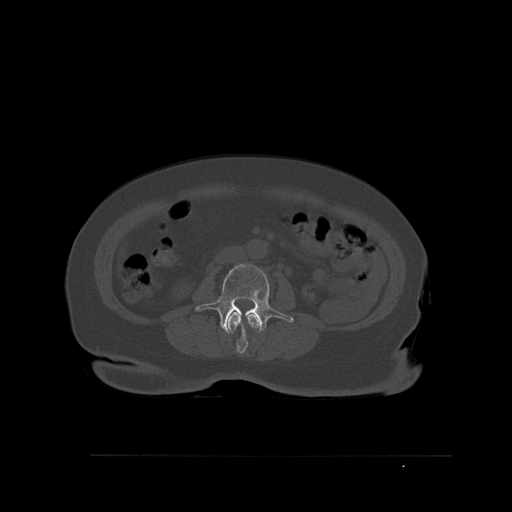
CT including the spine, one axial slice. Position 231 of 527 along the scan axis. Bone window (W 1800 / L 400 HU). 512 × 512 image matrix, field of view 470 × 470 mm. Female patient, age 73 years. Case-level facts recorded for this patient, not image findings: primary cancer: breast; vertebrae with lytic lesions (as recorded): L2.
Annotated regions visible in this slice (semi-automatic segmentation, software-assisted and operator-edited):
- L2 vertebra: bounding box (x1, y1, x2, y2) in pixels: (227, 312, 259, 354)
- L3 vertebra: (195, 264, 294, 335)
- L4 vertebra: (258, 324, 260, 328)